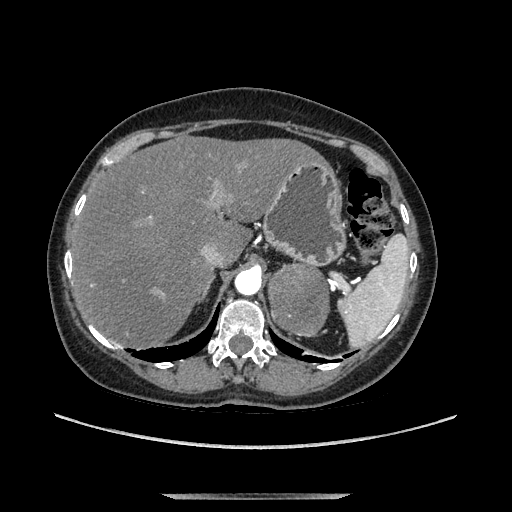
Contrast-enhanced abdominal CT, one axial slice. Position 97 of 169 along the scan axis. Soft-tissue window (W 400 / L 40 HU). 512 × 512 image matrix, field of view 400 × 400 mm. Female patient. Case-level facts recorded for this patient, not image findings: diagnosis: adrenocortical carcinoma; tumour side: left adrenal; tumour size at pathology: 9 cm; Ki-67 index: 2 %; stage (as recorded): 3.
Outlined on this slice (semi-automatically segmented with operator editing):
- mass: bounding box [x1, y1, x2, y2] px = [271, 266, 326, 333]